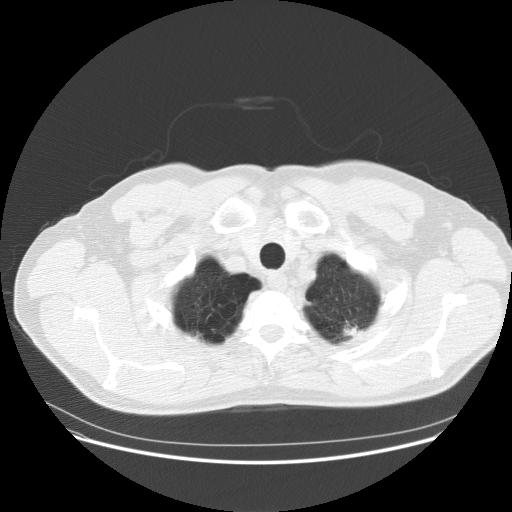
Low-dose screening chest CT, axial slice, first (baseline) screen, lung window (W 1500 / L -600 HU), 512 × 512 image matrix. Male participant, aged 61 years at enrolment. Current smoker at enrolment.
- Expert reader's lesion annotation, box from (x=317, y=306) to (x=381, y=355) px.
- Reader record for this screening exam (exam-level; its link to the box is not recorded): non-calcified nodule or mass ≥4 mm, left upper lobe, 12 × 6 mm, poorly defined margins, soft tissue attenuation.
- Official screen result: positive, change unspecified: nodule(s) >= 4 mm or enlarging nodule(s), mass(es), or other non-specific abnormalities suspicious for lung cancer.
- Lung cancer was diagnosed 317 days after this screen: adenocarcinoma, NOS, left upper lobe, poorly differentiated (G3), stage IIIA (AJCC 6th edition), 30 mm at pathology.